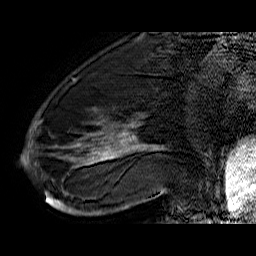
Breast MRI (dynamic contrast-enhanced), one sagittal slice; slice 19 of 60 in the series (ordered by position); dynamic contrast-enhanced series, time point 2 of 6 at this slice position (early post-contrast); 1.5 T; TE 6.4 ms, TR 32.9 ms; 4 mm slice thickness; 256 × 256 image matrix, field of view 200 × 200 mm. Female patient. Case-level facts recorded for this patient, not image findings: setting: breast cancer imaged before/during neoadjuvant chemotherapy; receptor status: HR-positive, HER2-negative.
Structures marked on this image (semi-automatic segmentation, software-assisted and operator-edited):
- analysis volume of interest (the breast-tissue region the enhancement analysis was run in; not a lesion): bounding box [x1, y1, x2, y2] px = [45, 74, 176, 210]
- tumour enhancement mask (voxels above the 100 % enhancement threshold inside the analysis volume of interest): [45, 123, 166, 207]